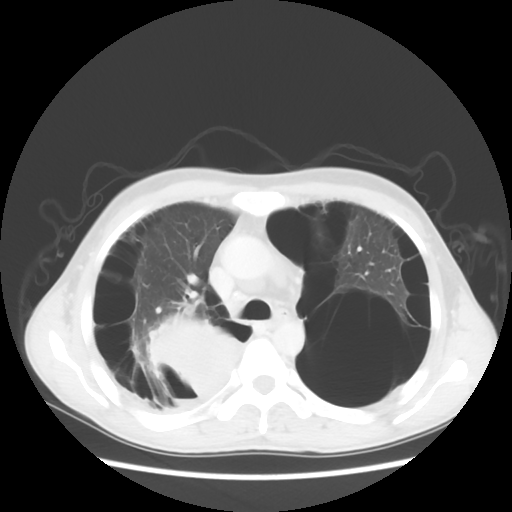
Chest CT, one axial slice; position 37 of 56 along the scan axis; reconstruction kernel STANDARD; 140 kVp; lung window (W 1500 / L -600 HU); 5 mm slice thickness; 512 × 512 image matrix, field of view 351 × 351 mm. Male patient, age 41 years. Case-level facts recorded for this patient, not image findings: clinical TNM (as recorded): T4 N0 M1a.
Outlined on this slice (rectangle marked by the reading radiologist):
- lung tumour (recorded histology: large cell carcinoma): bounding box [x1, y1, x2, y2] px = [142, 313, 253, 412]